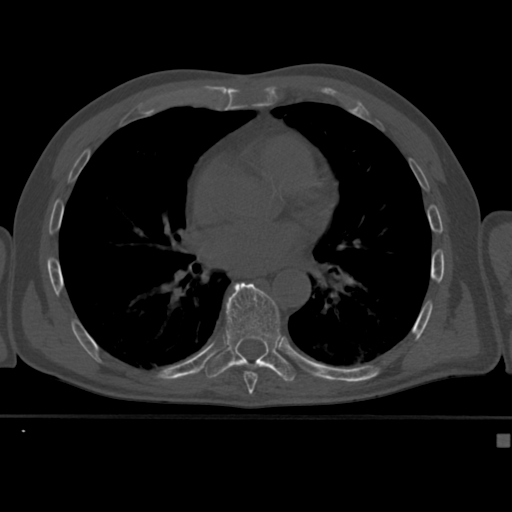
CT including the spine, one axial slice; reconstruction kernel Br40s; 120 kVp; bone window (W 1800 / L 400 HU); 1.5 mm slice thickness; 512 × 512 image matrix, field of view 337 × 337 mm. Male patient, age 64 years. From the clinical record (not read from this slice): primary cancer: uterus.
Structures marked on this image (semi-automatically segmented with operator editing):
- T8 vertebra: bounding box [x1, y1, x2, y2] px = [243, 371, 258, 382]
- T9 vertebra: [204, 282, 297, 382]